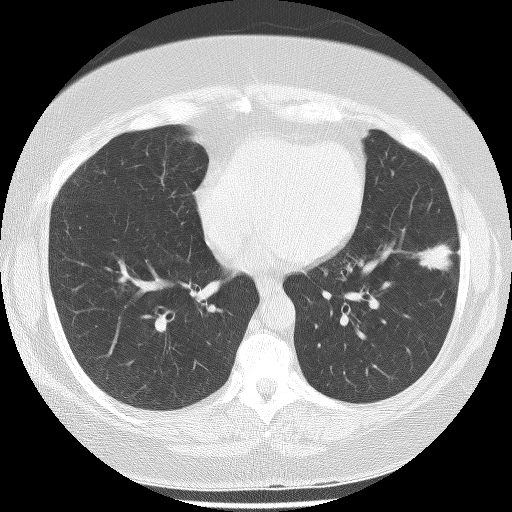
Low-dose screening chest CT, one axial slice. Position 105 of 233 along the scan axis. Reconstruction kernel BONE. 120 kVp. Lung window (W 1500 / L -600 HU). 512 × 512 image matrix, field of view 340 × 340 mm.
Outlined on this slice (manually delineated by an expert):
- lesion 1 (tumor, lower lobe of left lung): box from (x=417, y=242) to (x=453, y=273) px